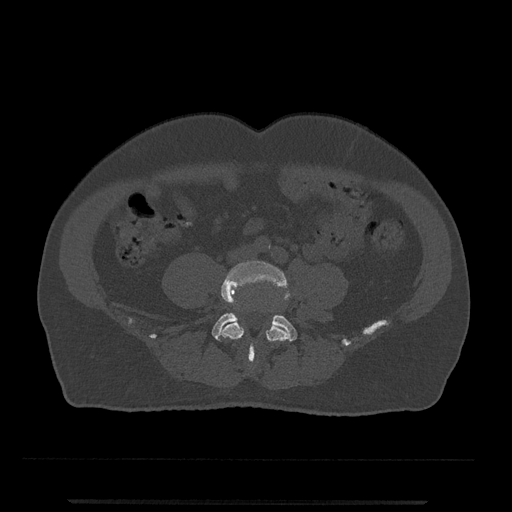
CT including the spine, one axial slice. Position 105 of 797 along the scan axis. Reconstruction kernel Br40s/3. 120 kVp. Bone window (W 1800 / L 400 HU). 0.5 mm slice thickness. 512 × 512 image matrix, field of view 419 × 419 mm. Patient: male, 63 years. Case-level facts recorded for this patient, not image findings: primary cancer: prostate.
Annotated regions visible in this slice (semi-automatically segmented with operator editing):
- L4 vertebra: box from (x=220, y=260) to (x=293, y=365) px
- L5 vertebra: (x=212, y=313)–(x=297, y=359)